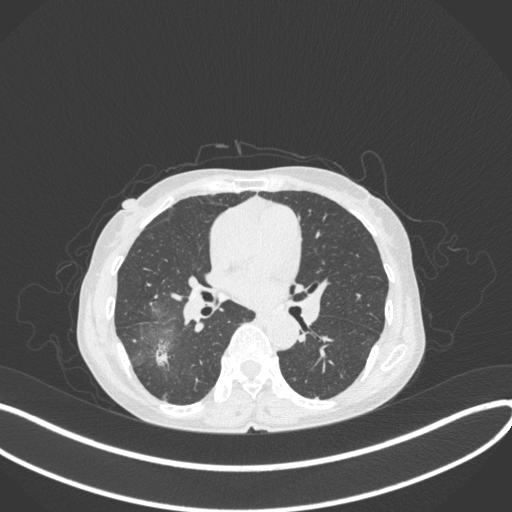
Chest CT, one axial slice. Position 207 of 379 along the scan axis. Reconstruction kernel B31f. 120 kVp. Lung window (W 1500 / L -600 HU). 1 mm slice thickness. 512 × 512 image matrix. Female patient, age 69 years. Case-level facts recorded for this patient, not image findings: clinical TNM (as recorded): T1b N0 M0.
Structures marked on this image (bounding box drawn by a radiologist):
- lung tumour (recorded histology: adenocarcinoma): bounding box <148,339,177,371> (left, top, right, bottom; pixels)